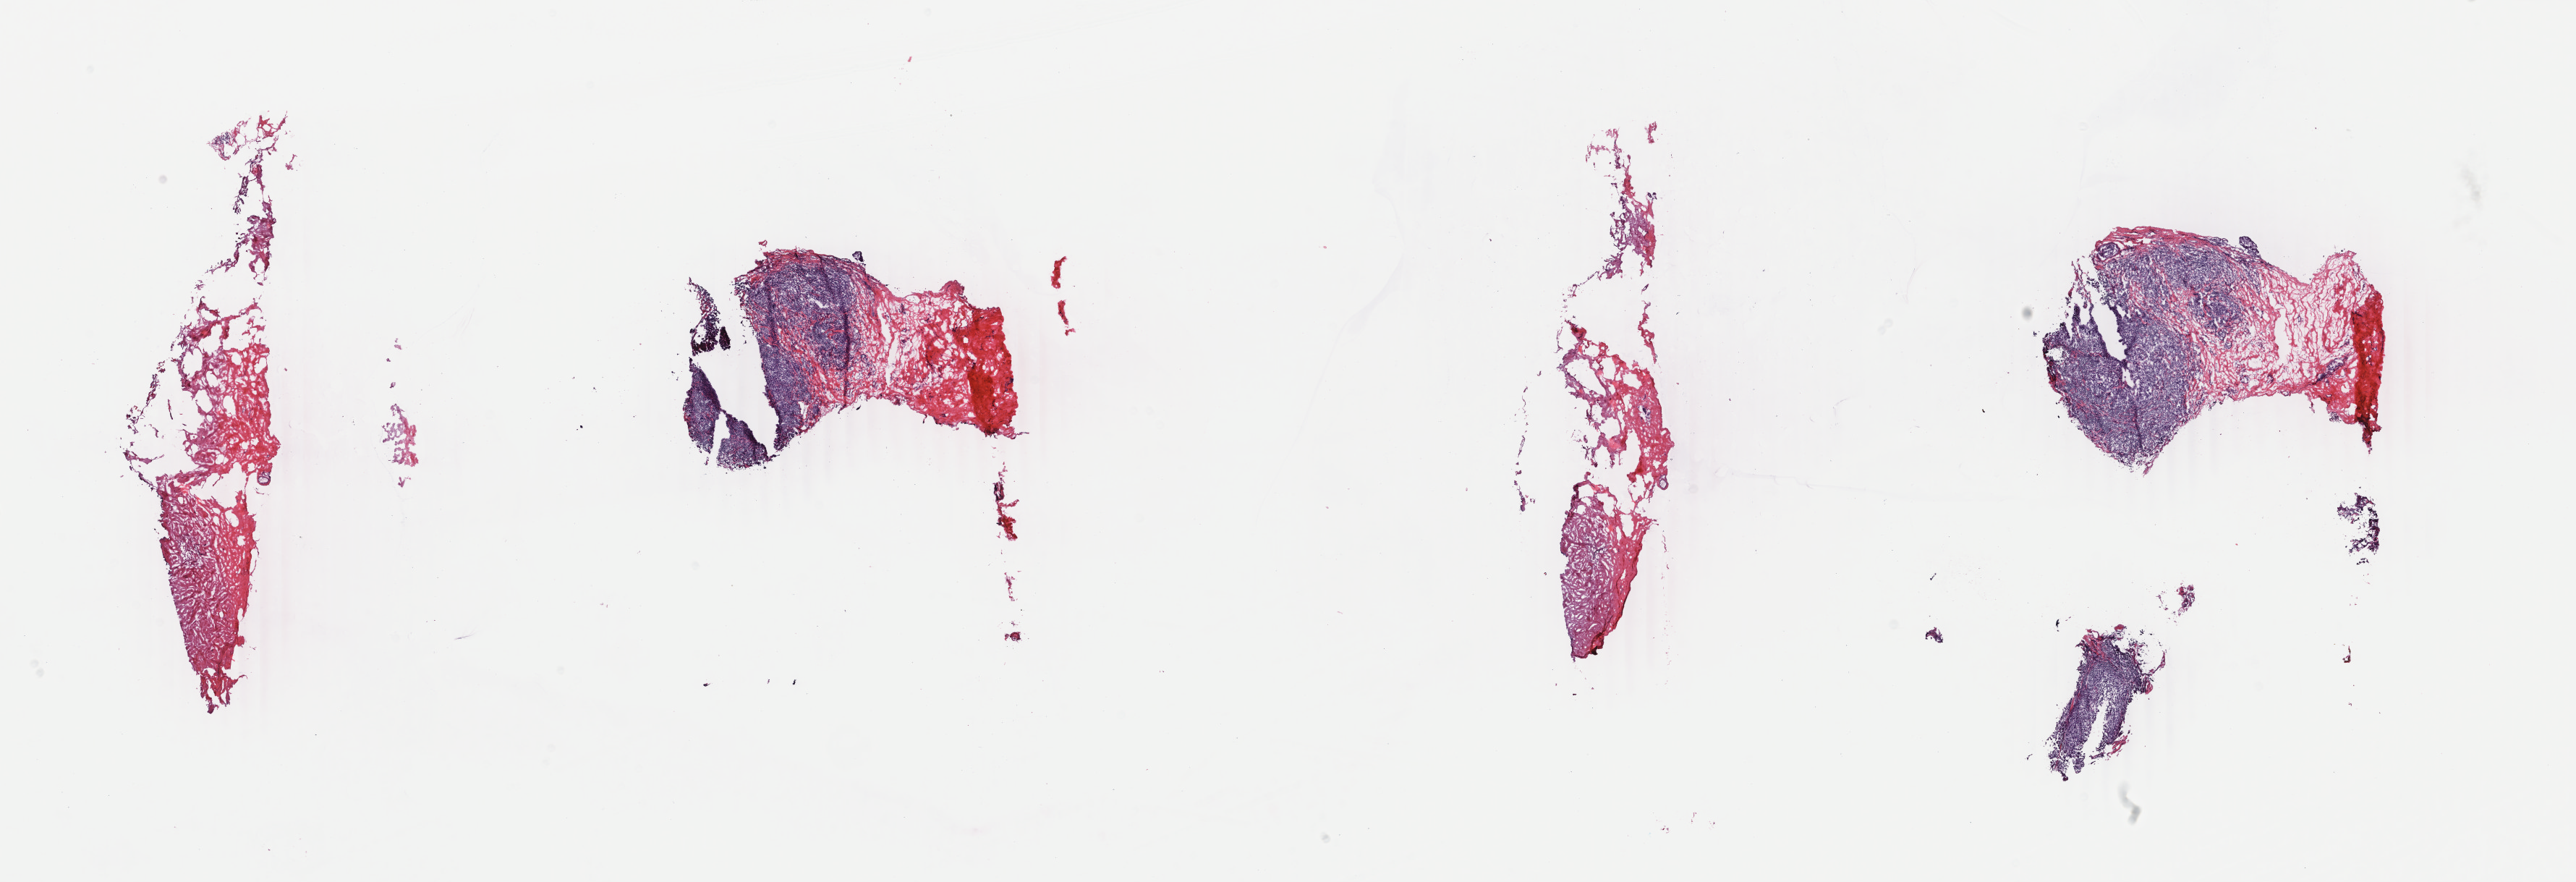
Digitized H&E-stained tissue section (whole slide) — whole scanned area (about 28.3 x 9.7 mm) shown as a low-resolution overview. Frozen section from the bottom of the tissue portion. Breast, primary tumour sample. Patient: female, age at initial diagnosis 62 years. Pathologist review of this section (percent, as recorded): tumour cells 70%, tumour nuclei 90%, normal cells 0%, stromal cells 28%, necrosis 2%. Infiltration values recorded for this section: lymphocyte infiltration 12%, monocyte infiltration 0%, neutrophil infiltration 1%.
- TNM: T1c N1a M0
- AJCC pathologic stage: IIA (6th edition)
- diagnosis: Infiltrating duct carcinoma, NOS